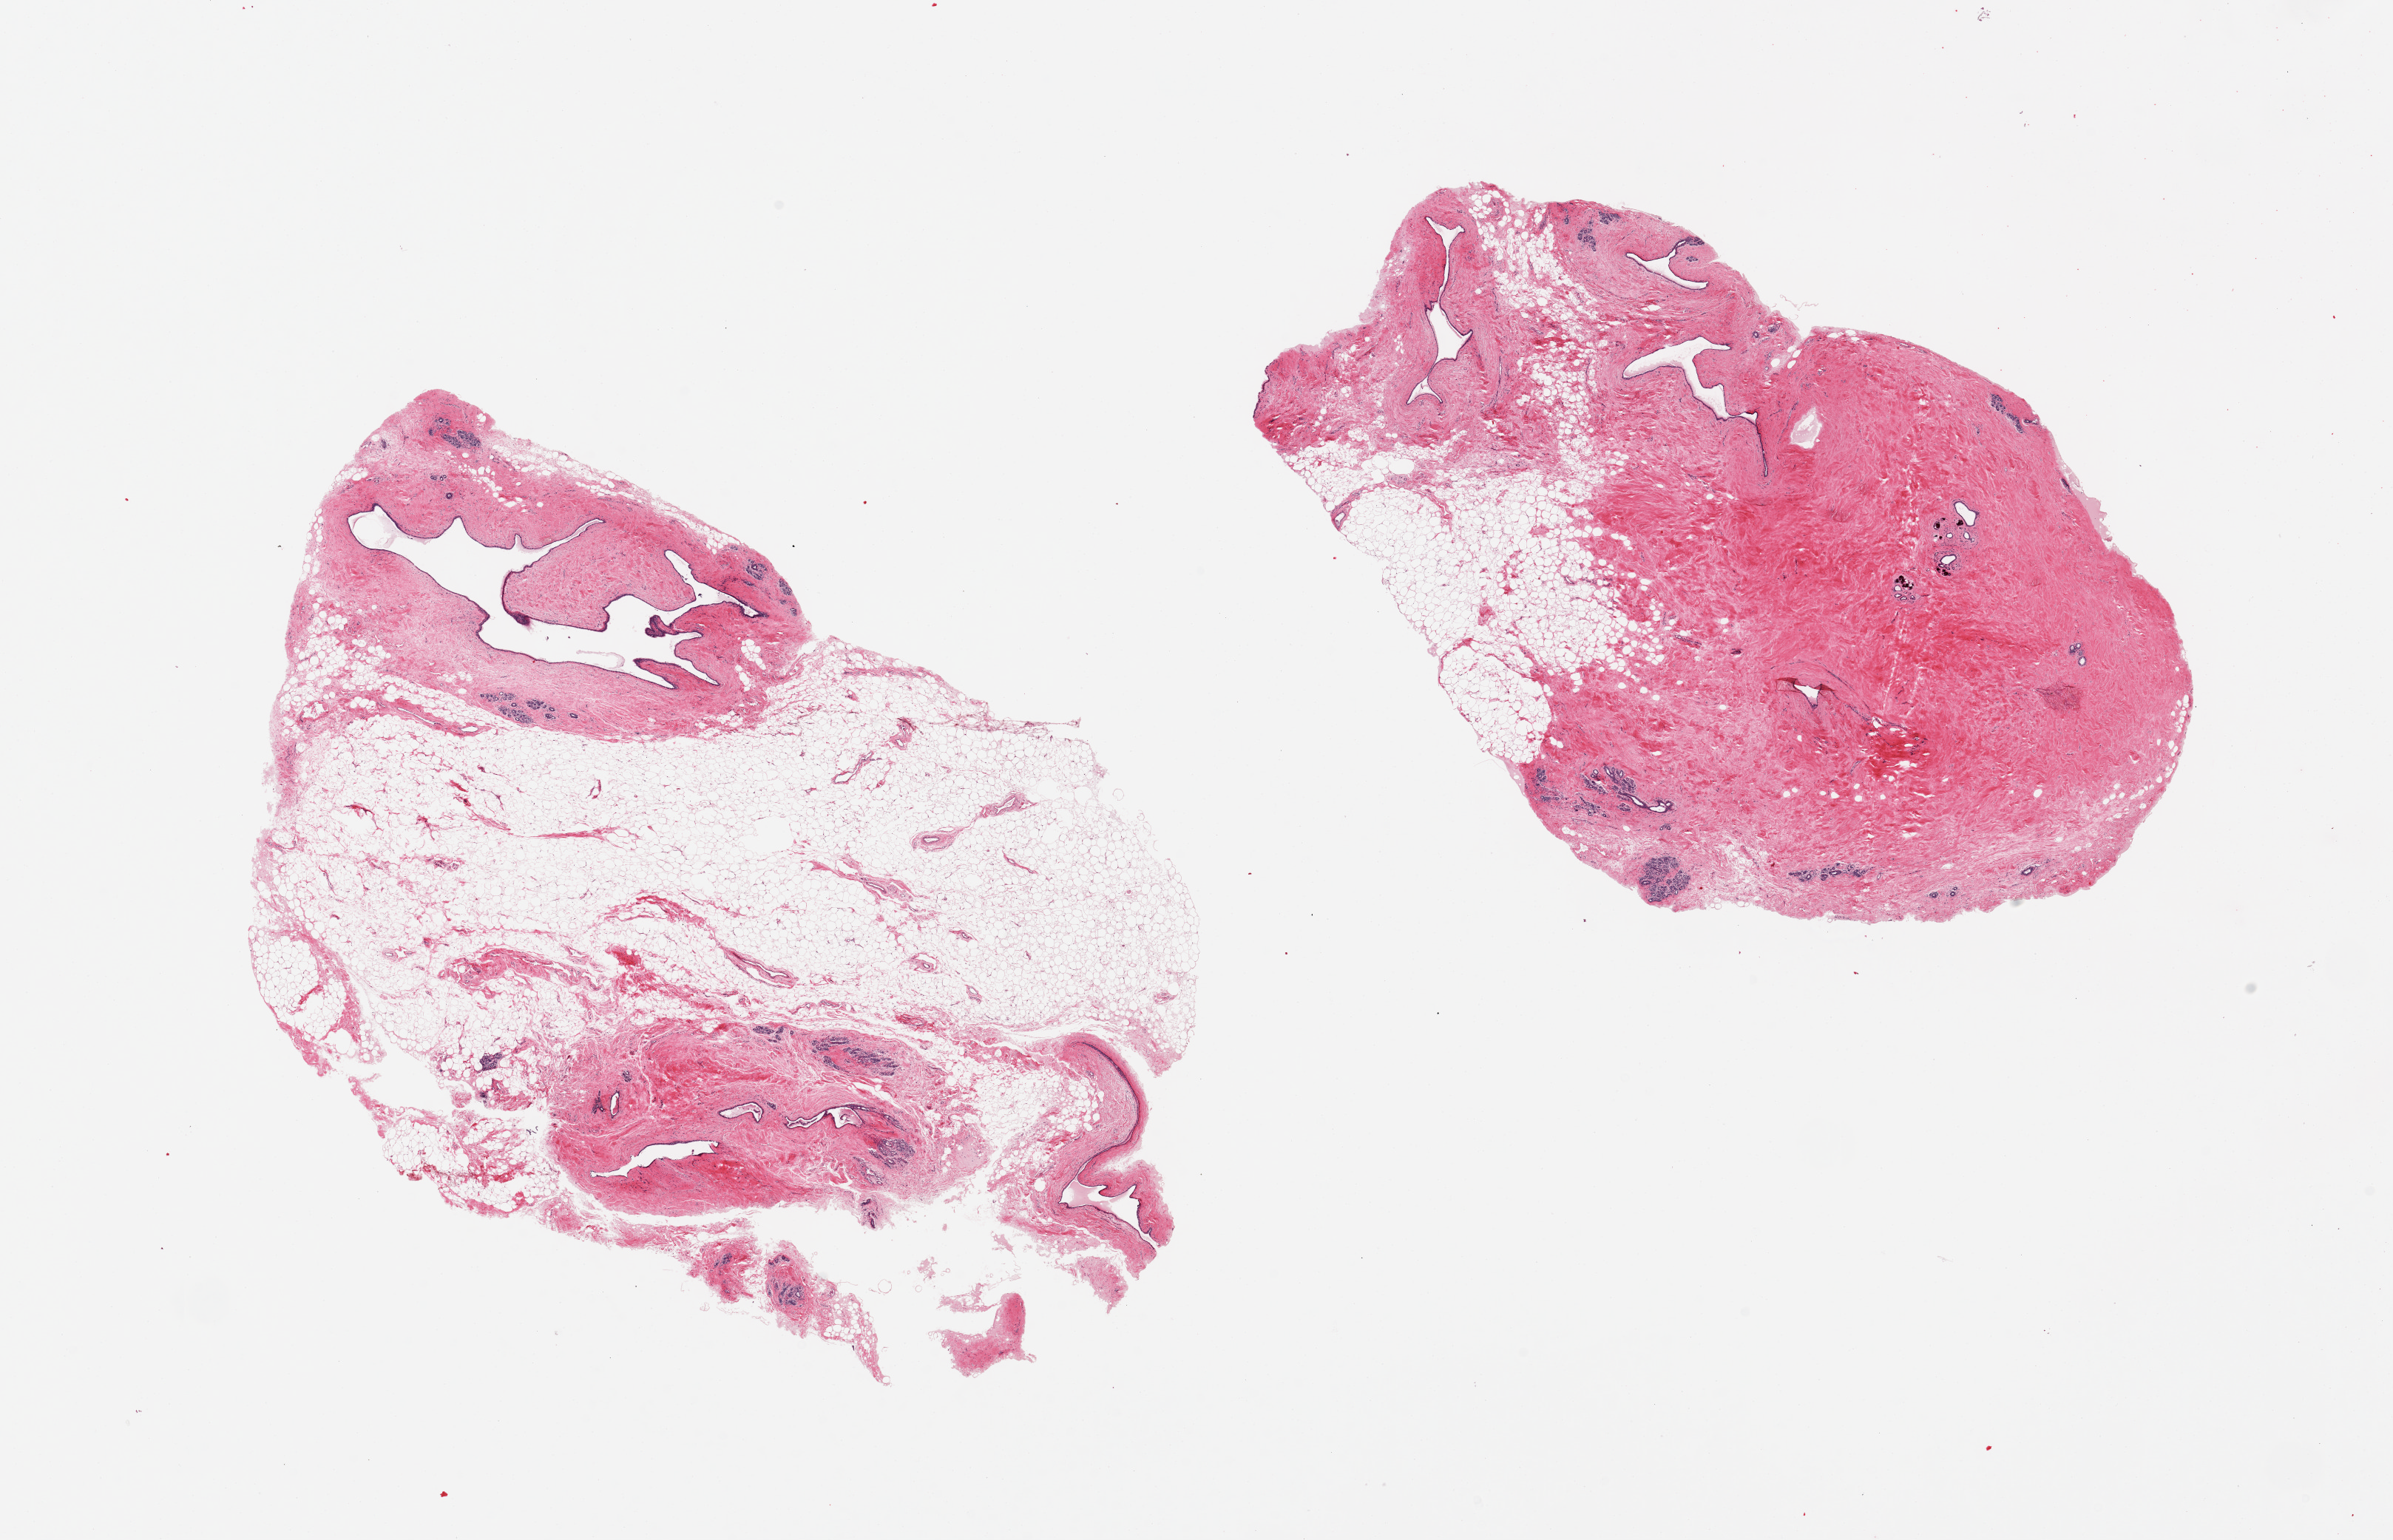
Haematoxylin and eosin whole-slide image — shown as a low-resolution overview of the whole scanned area (about 25.6 x 16.5 mm), PAXgene-fixed paraffin-embedded (PFPE) section, sampled site (target tissue): breast, tissue donor sample. Female donor.
* pathologist's review note for this sample: 2 pieces, fibrocystic changes; TDLUs, dilated ducts